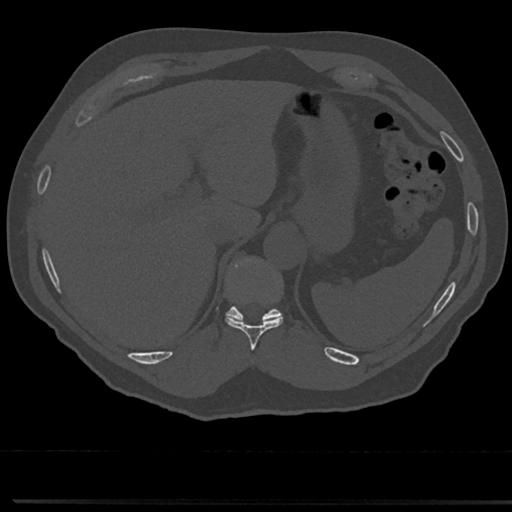
CT including the spine, one axial slice; position 238 of 817 along the scan axis; 120 kVp; bone window (W 1800 / L 400 HU); 0.5 mm slice thickness; 512 × 512 image matrix. Patient: male, 61 years. Case-level facts recorded for this patient, not image findings: primary cancer: prostate.
Structures marked on this image (semi-automatically segmented with operator editing):
- T10 vertebra: bounding box (x1, y1, x2, y2) in pixels: (226, 261, 283, 348)
- T11 vertebra: (227, 261, 280, 321)